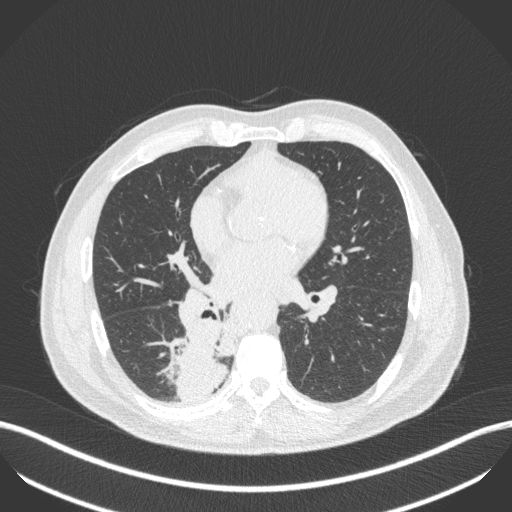
Chest CT, one axial slice. Position 226 of 451 along the scan axis. Reconstruction kernel B31f. 100 kVp. Lung window (W 1500 / L -600 HU). 1 mm slice thickness. 512 × 512 image matrix, field of view 400 × 400 mm. Patient: male, 61 years. From the clinical record (not read from this slice): clinical TNM (as recorded): T1 N0 M0.
Annotated regions visible in this slice (bounding box drawn by a radiologist):
- lung tumour (recorded histology: small cell carcinoma): box from (x=166, y=317) to (x=226, y=400) px